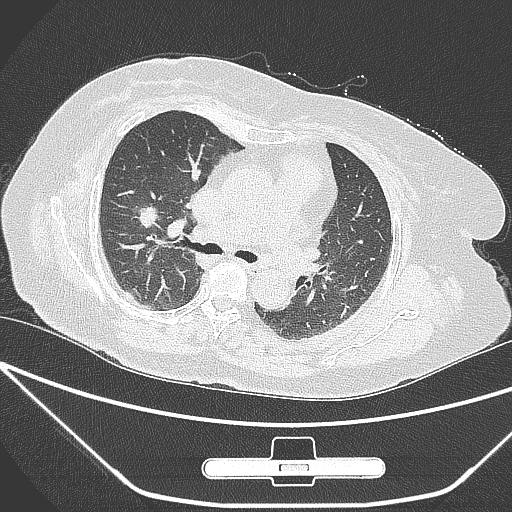
Chest CT, one axial slice; slice 164 of 245 in the series (ordered by position); lung window (W 1500 / L -600 HU); 1 mm slice thickness; 512 × 512 image matrix, field of view 365 × 365 mm. Female patient, age 65 years. From the clinical record (not read from this slice): clinical TNM (as recorded): T1c N0 M0.
Annotated regions visible in this slice (rectangle marked by the reading radiologist):
- lung tumour (recorded histology: adenocarcinoma): bounding box [x1, y1, x2, y2] px = [134, 205, 160, 234]